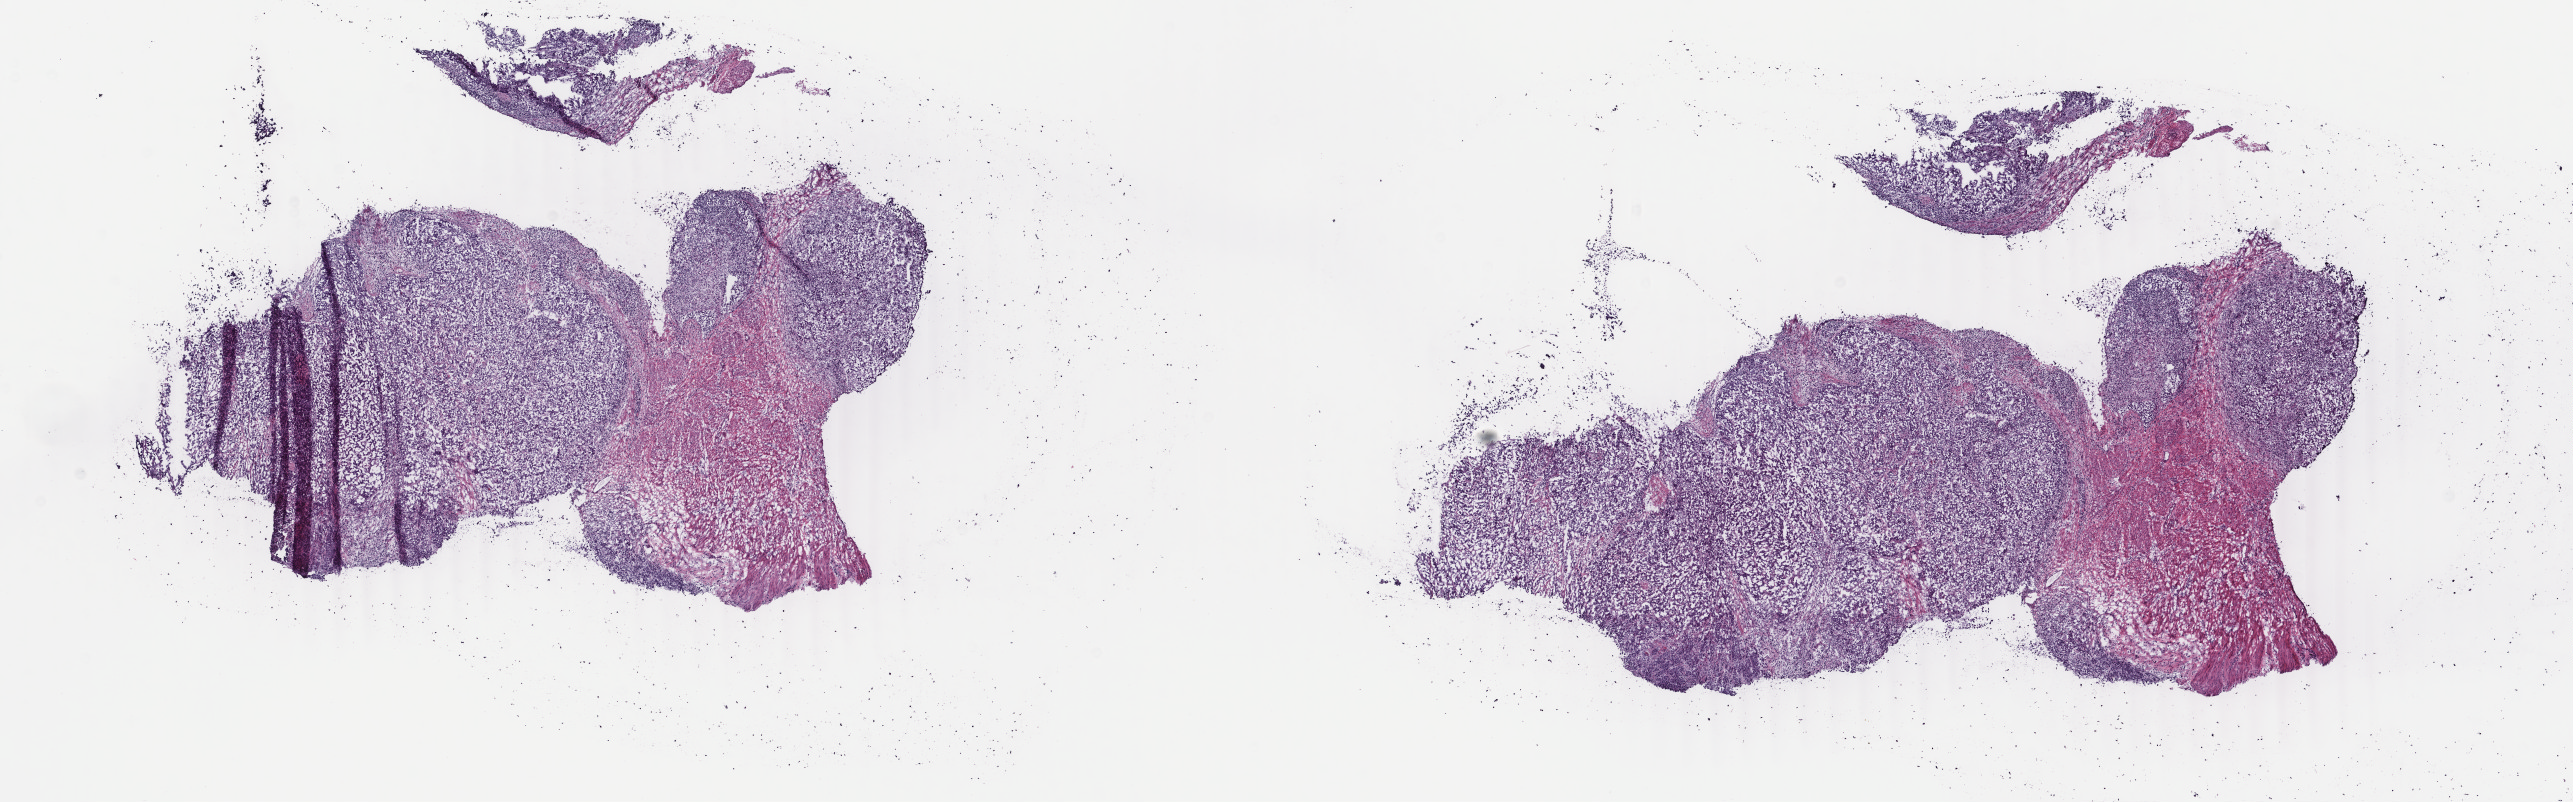
Hematoxylin and eosin (H&E) stained whole-slide image, a low-resolution overview of the entire scanned area, about 20.5 x 6.4 mm; frozen section; uterus, primary tumour sample. Female, age 66 years at initial diagnosis. Histologic grade: G3 (poorly differentiated). Slide review estimates, as recorded: tumour cells 70%, tumour nuclei 80%, normal cells 20%, stromal cells 0%, necrosis 10%. Inflammatory infiltration, as recorded: lymphocyte infiltration 20%, monocyte infiltration 0%, neutrophil infiltration 10%.
FIGO stage: IIIC2. Pathologic diagnosis: Carcinoma, undifferentiated, NOS (endometrium).